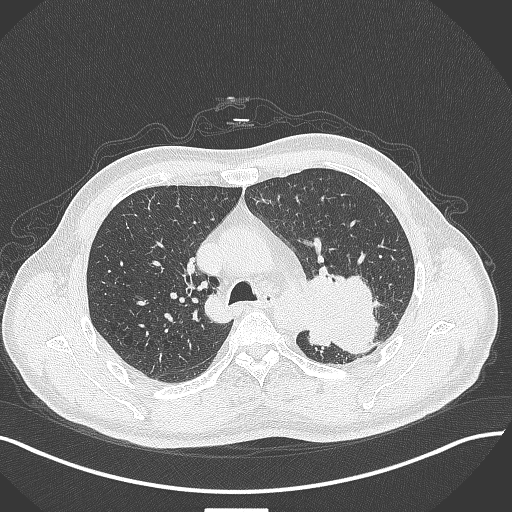
Chest CT, one axial slice; slice 292 of 429 in the series (ordered by position); reconstruction kernel B70f; 120 kVp; lung window (W 1500 / L -600 HU); 1 mm slice thickness; 512 × 512 image matrix, field of view 400 × 400 mm. Male patient, age 55 years. Case-level facts recorded for this patient, not image findings: clinical TNM (as recorded): T3 N0 M1c.
Outlined on this slice (rectangle marked by the reading radiologist):
- lung tumour (recorded histology: adenocarcinoma): box from (x=305, y=269) to (x=383, y=354) px